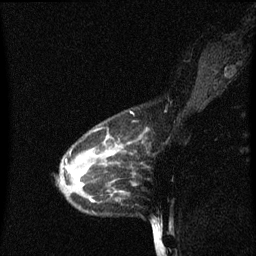
Breast MRI (dynamic contrast-enhanced), one sagittal slice. Dynamic contrast-enhanced series, image 2 of 3 at this slice position (ordered by acquisition). 1.5 T. TE 4.2 ms, TR 8.4 ms. 256 × 256 image matrix, field of view 200 × 200 mm. Patient: female, 38 years. Case-level facts recorded for this patient, not image findings: setting: breast cancer imaged before/during neoadjuvant chemotherapy; receptor status: HR-positive, HER2-negative.
Annotated regions visible in this slice (semi-automatic segmentation, software-assisted and operator-edited):
- analysis volume of interest (the breast-tissue region the enhancement analysis was run in; not a lesion): bounding box [x1, y1, x2, y2] px = [58, 126, 137, 205]
- tumour enhancement mask (voxels above the 70 % enhancement threshold inside the analysis volume of interest): [68, 168, 71, 171]